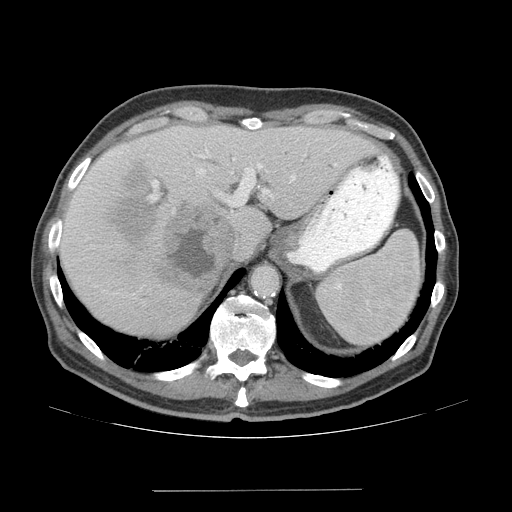
Contrast-enhanced abdominal CT (liver protocol), one axial slice. Slice 49 of 77 in the series (ordered by position). Reconstruction kernel STANDARD. 140 kVp. Soft-tissue window (W 400 / L 40 HU). 512 × 512 image matrix, field of view 400 × 400 mm. Case-level facts recorded for this patient, not image findings: diagnosis: hepatocellular carcinoma (patient treated with transarterial chemoembolisation; whether this scan precedes or follows treatment is not stated here); TNM stage (as recorded): Stage-IVA.
Structures marked on this image (semi-automatic segmentation, software-assisted and operator-edited):
- liver parenchyma outside the tumour (the mass and vessels are separate outlines, so this box may not span the whole liver): bounding box (x1, y1, x2, y2) in pixels: (60, 124, 376, 336)
- mass: (103, 161, 235, 296)
- liver vessels: (89, 139, 337, 200)